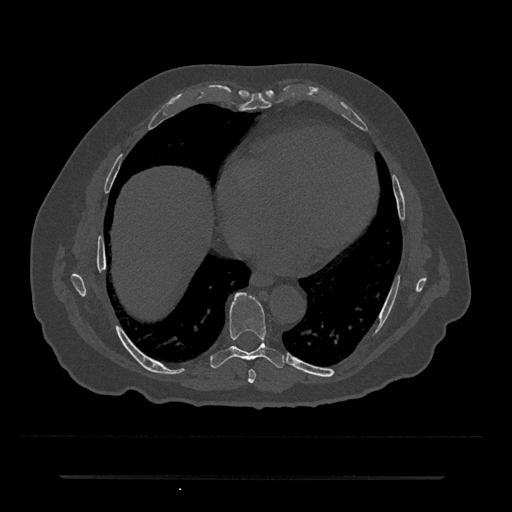
CT including the spine, one axial slice; position 336 of 797 along the scan axis; reconstruction kernel Br40s/3; bone window (W 1800 / L 400 HU); 0.5 mm slice thickness; 512 × 512 image matrix. Patient: male, 69 years. Case-level facts recorded for this patient, not image findings: primary cancer: prostate.
Outlined on this slice (semi-automatically segmented with operator editing):
- T7 vertebra: bounding box <248,369,256,383> (left, top, right, bottom; pixels)
- T8 vertebra: <211,293,285,369>